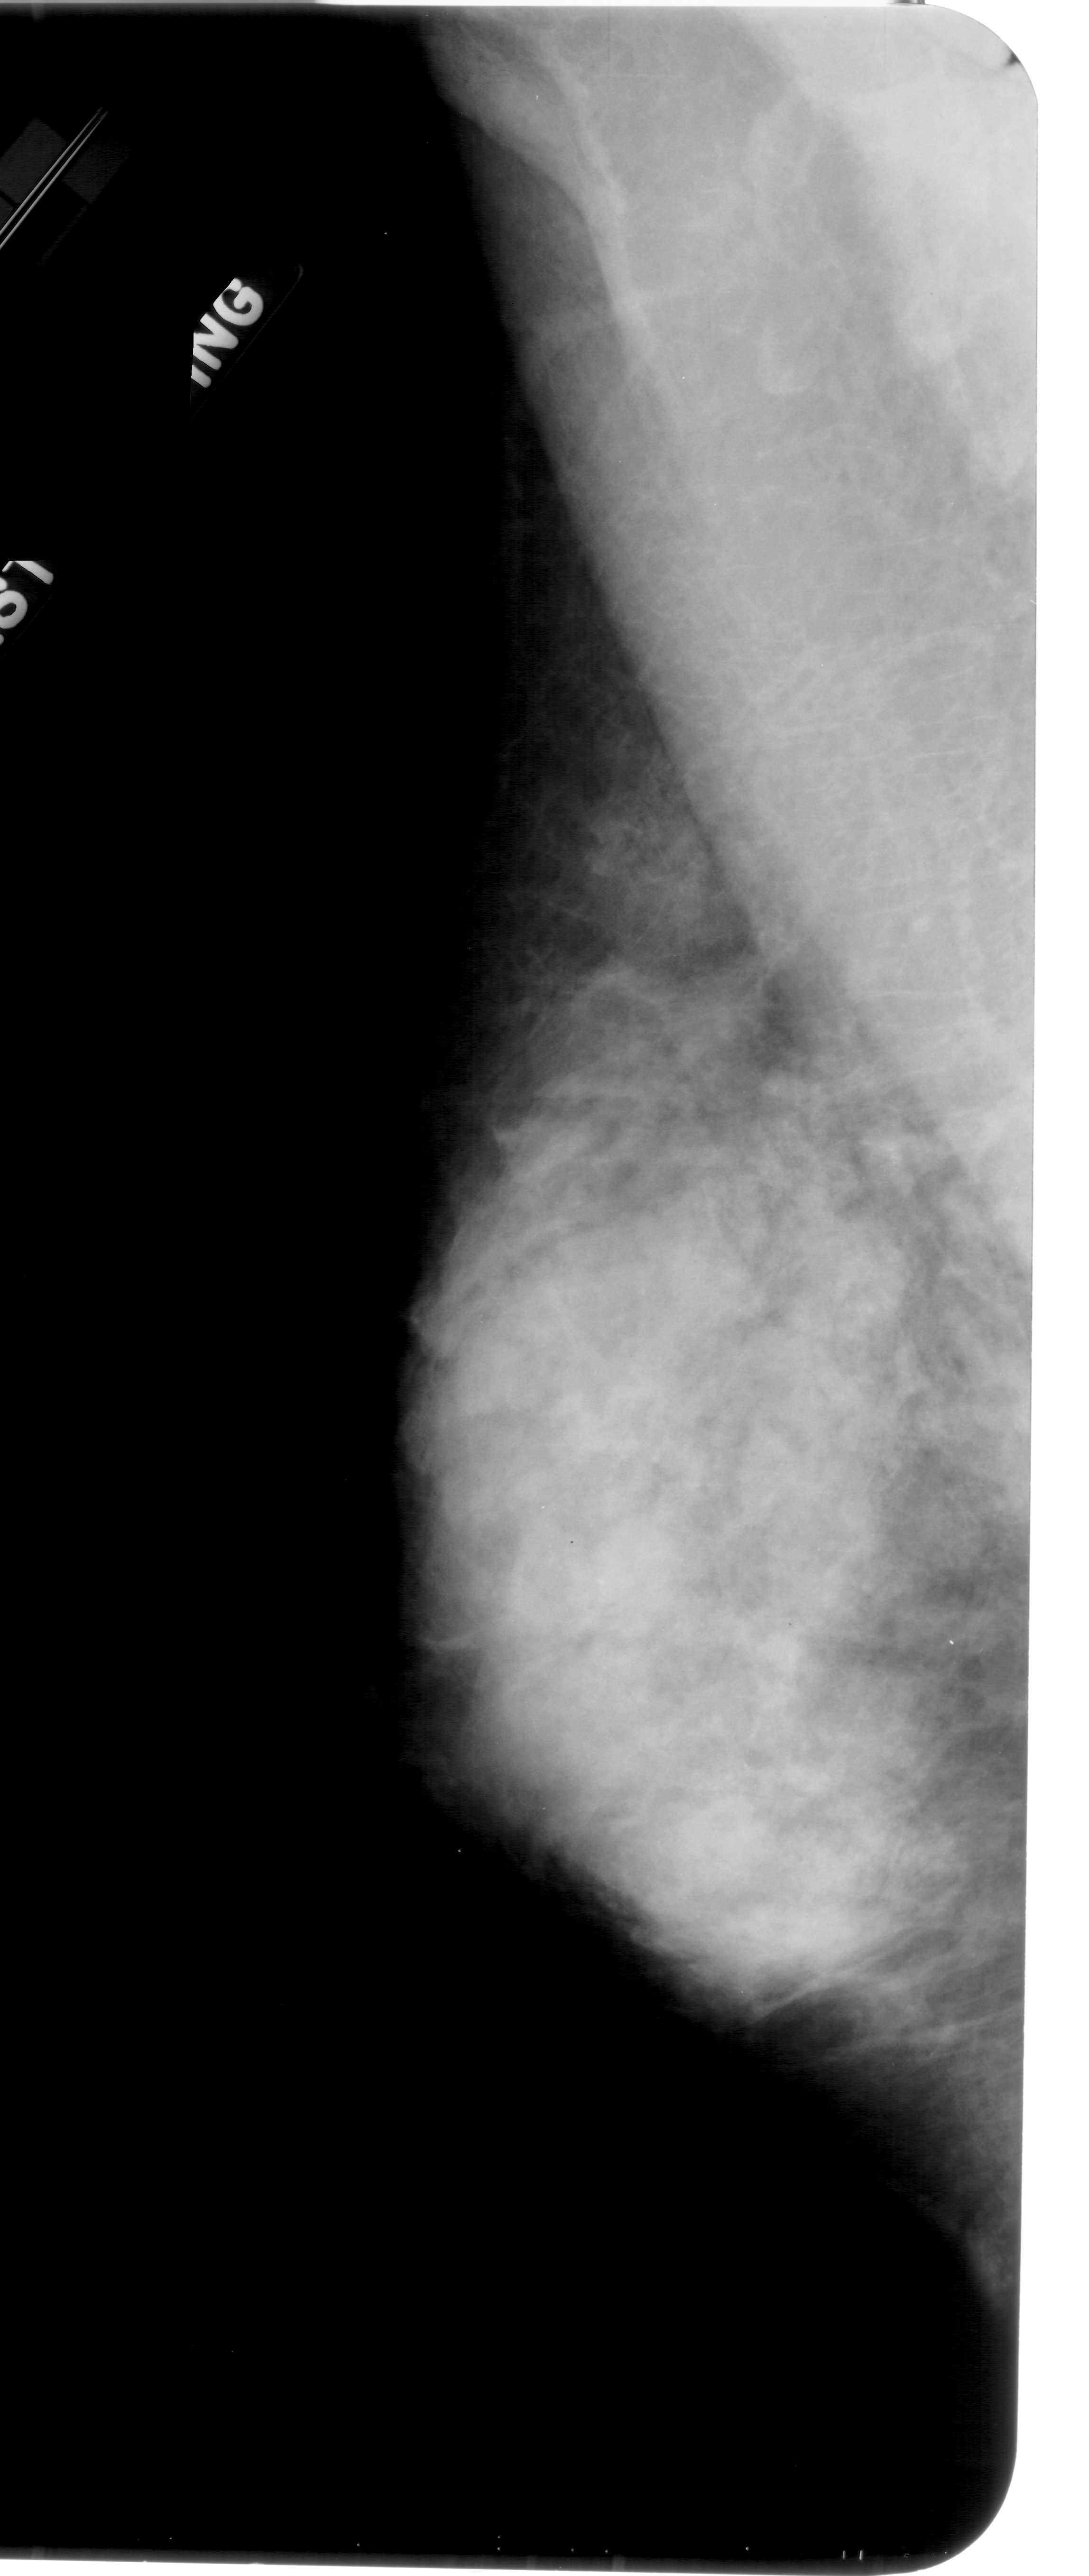
Digitized screen-film mammogram, left breast, MLO view.
- Marked findings (only marked abnormalities are described; nothing is implied about the rest of the image): calcifications, morphology pleomorphic, distribution clustered; BI-RADS assessment category 4; pathology result (as recorded, not read from the image): benign.